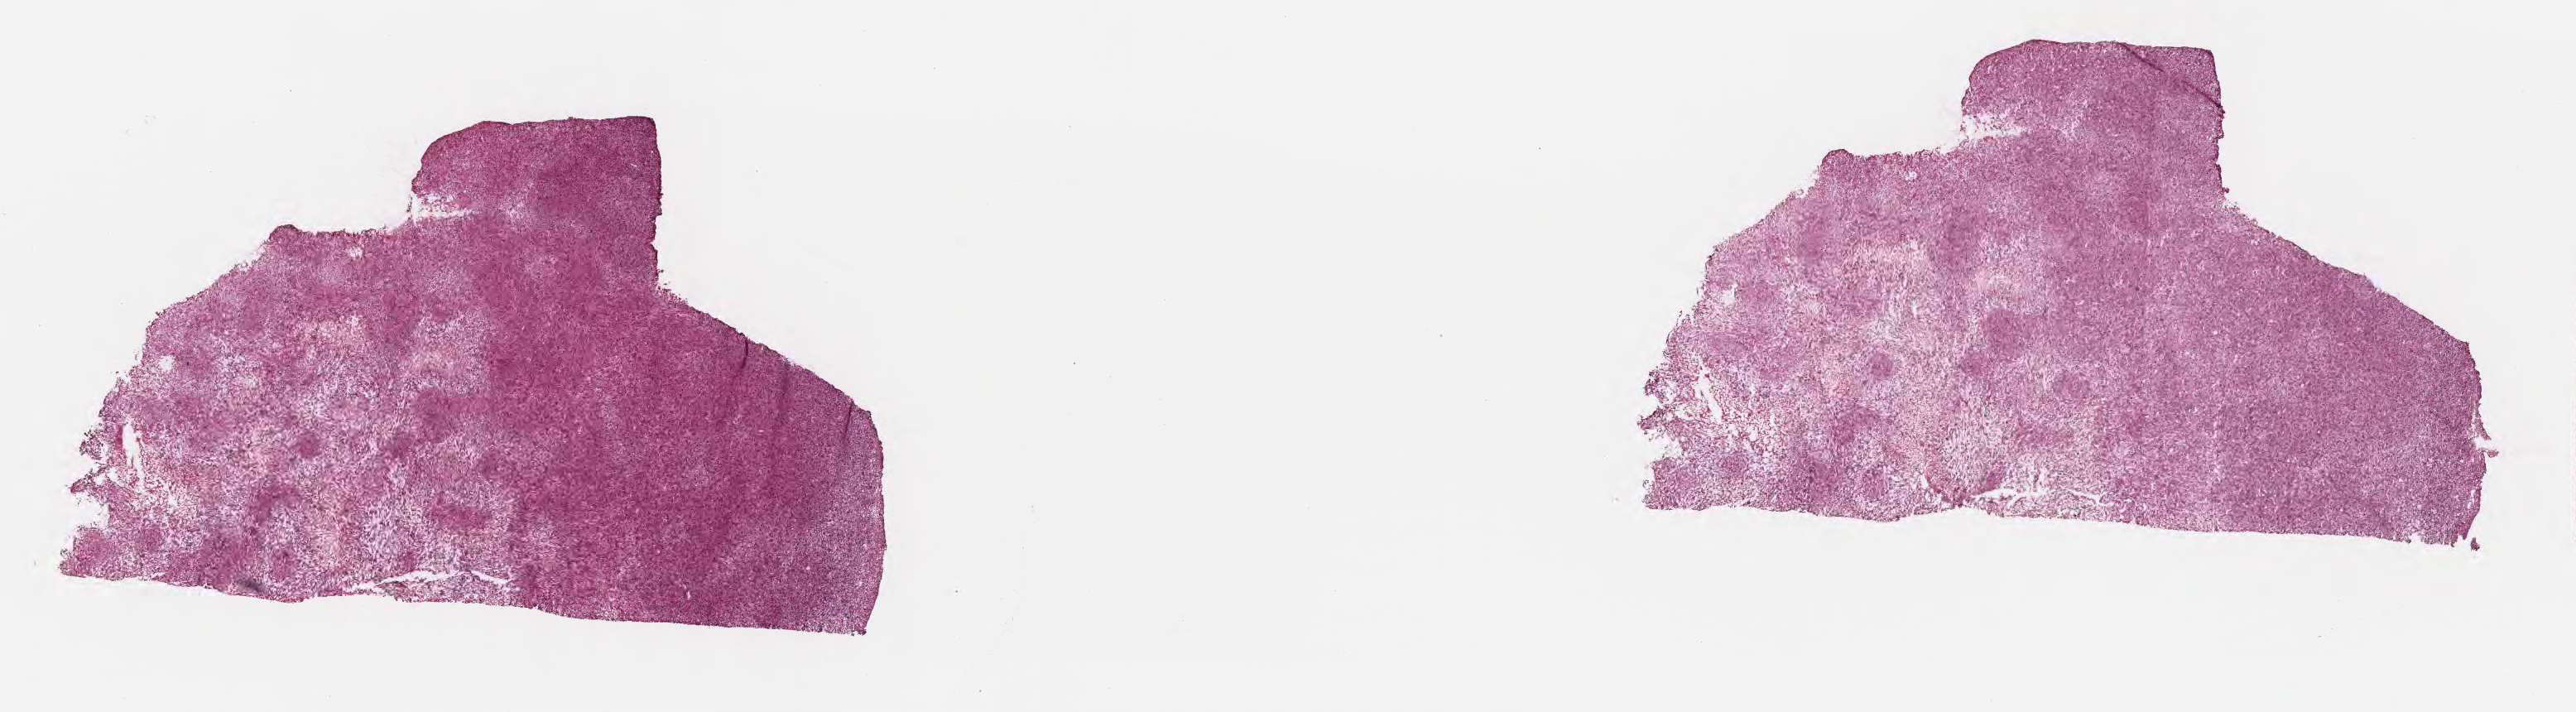
Haematoxylin and eosin whole-slide image — whole scanned area (about 25.2 x 7.0 mm) shown as a low-resolution overview, cryosection, specimen: metastatic tumor tissue, resected from brain. Male, age 76 years at initial diagnosis. Slide review estimates, as recorded: tumor cells 90%, tumor nuclei 95%, stromal cells 10%, necrosis 0%, normal cells 0%. Infiltration values recorded for this section: lymphocyte infiltration 0%, monocyte infiltration 0%, neutrophil infiltration 0%.
Section: top of the tissue portion. Patient diagnosis (primary): Spindle cell sarcoma.